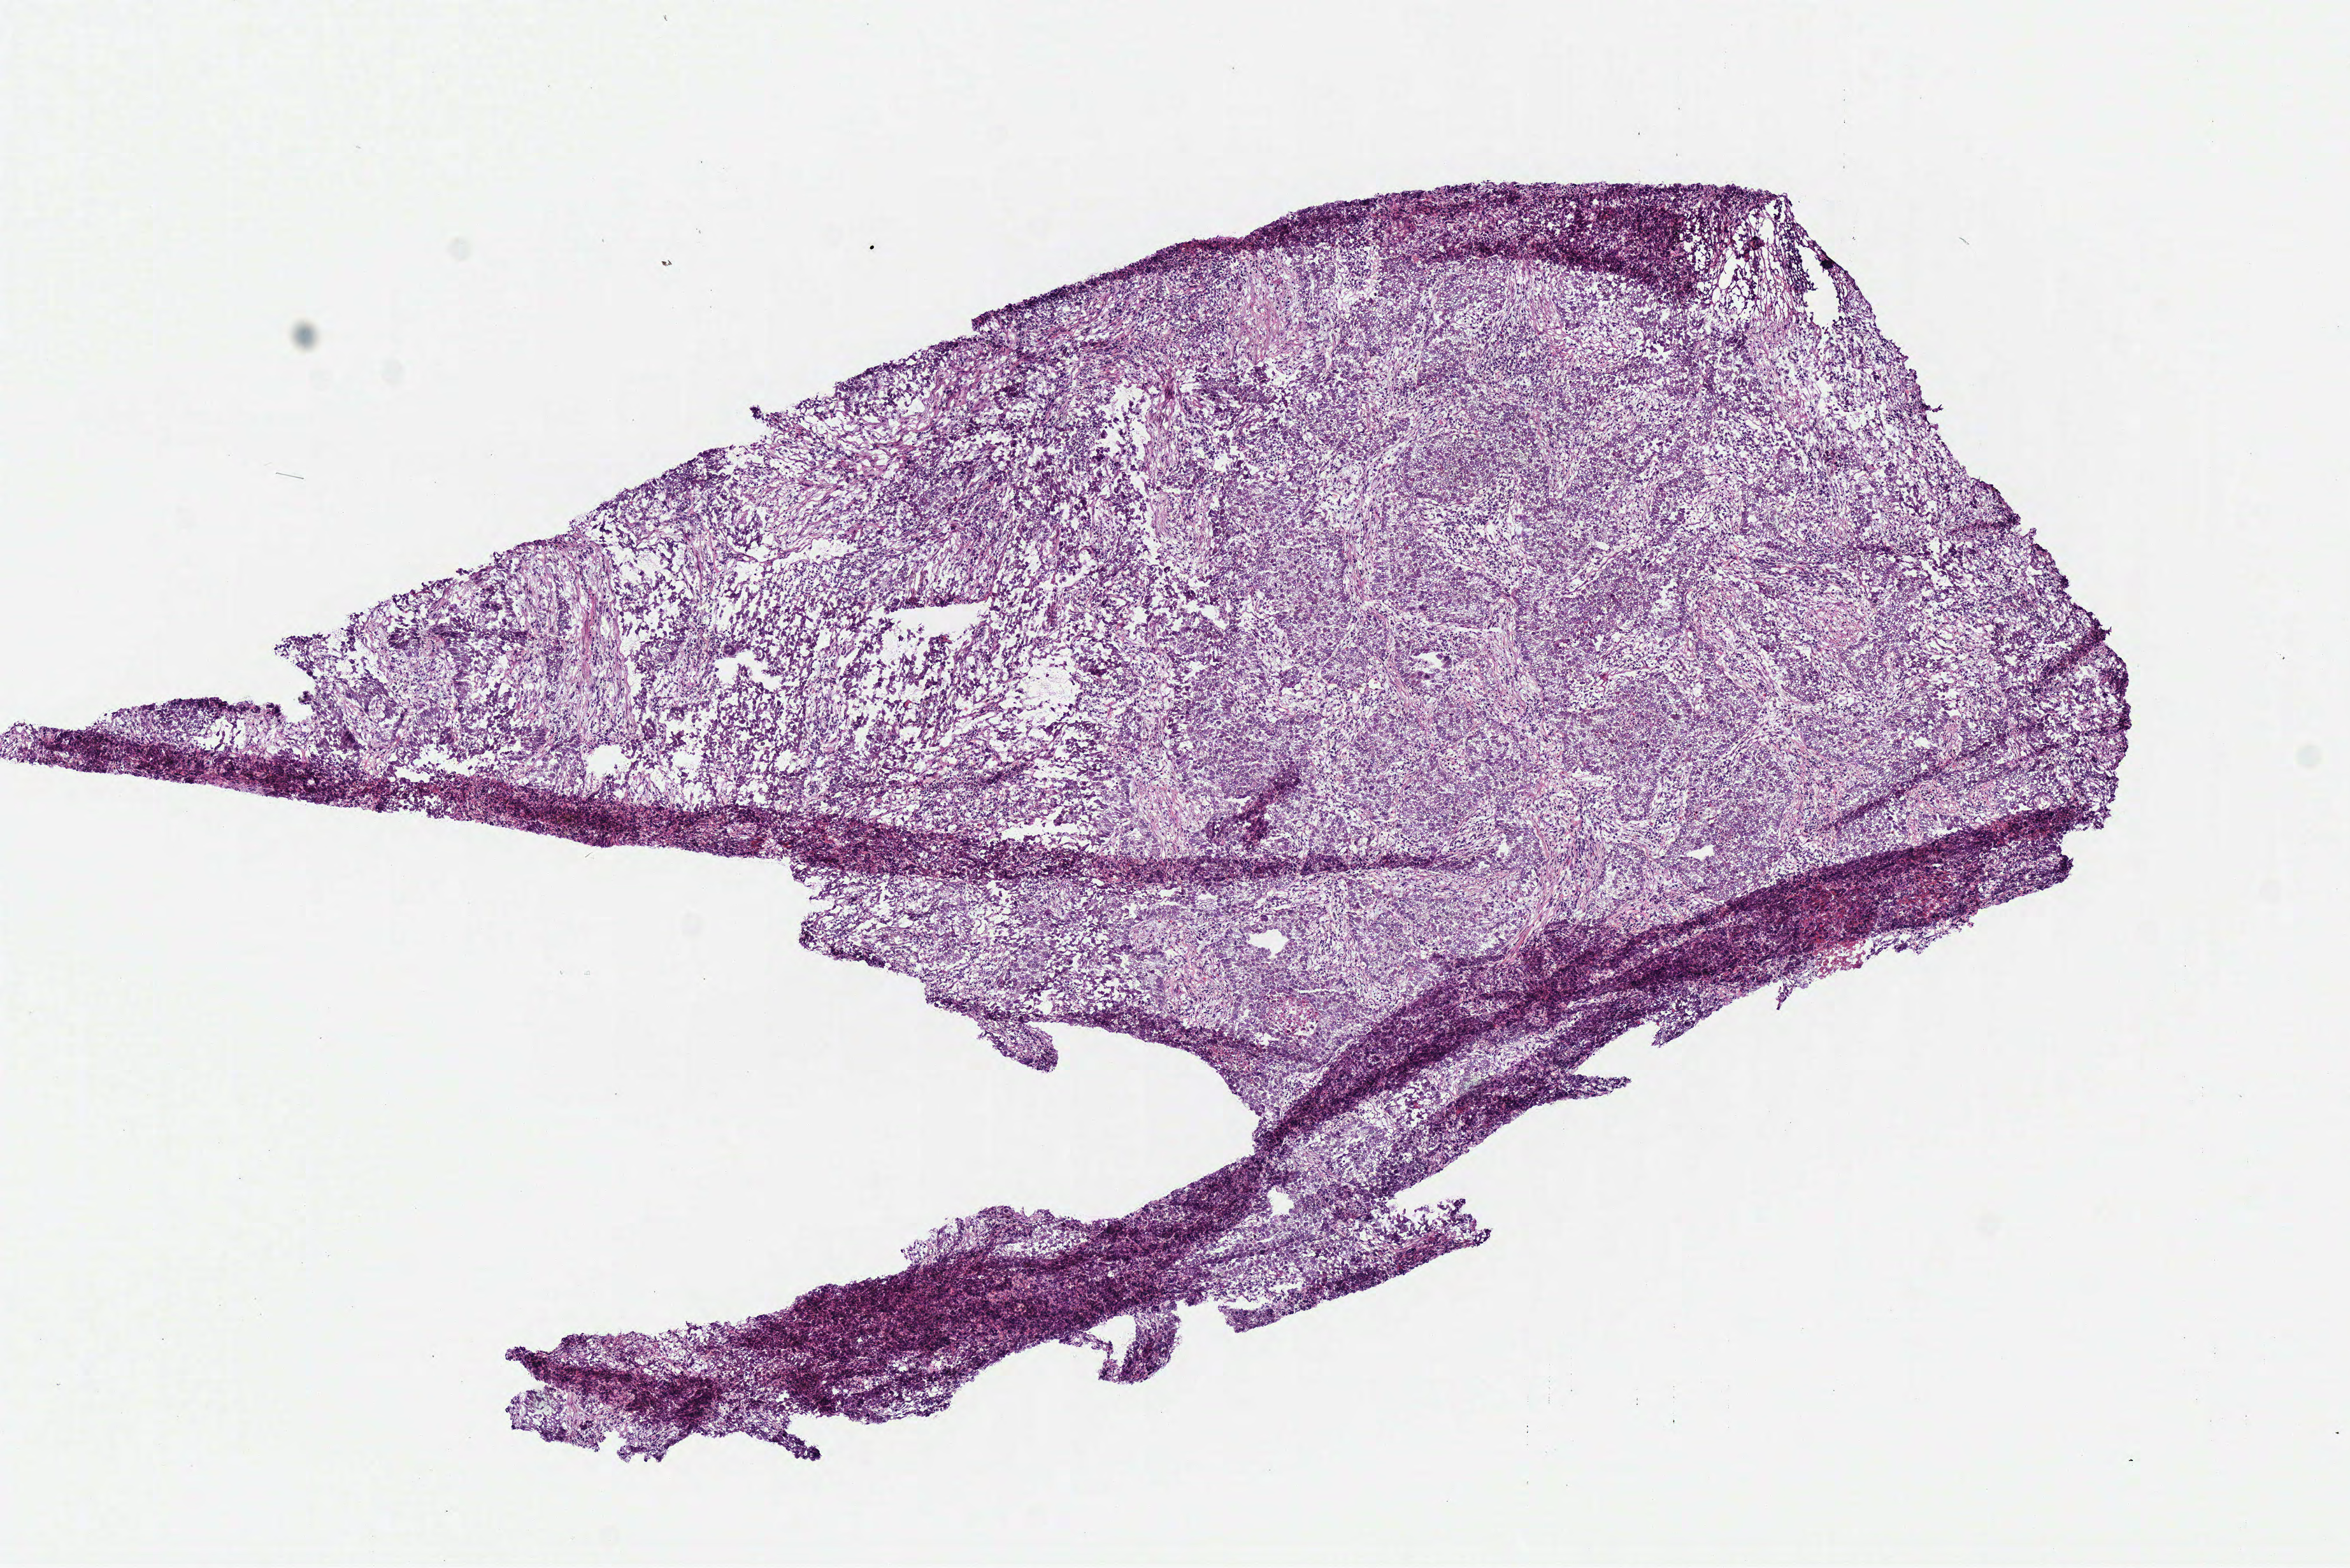
H&E whole-slide image, shown as a low-resolution overview of the whole scanned area (about 7.3 x 4.8 mm, from a 40x scan); frozen section; sample: primary tumour, lung. Patient sex: female. Pathologist review of this section (percent, as recorded): tumour cells 100%, tumour nuclei 80%, normal cells 0%, stromal cells 0%, necrosis 0%. Inflammatory infiltration, as recorded: lymphocyte infiltration 7%, monocyte infiltration 2%, neutrophil infiltration 7%.
- histologic diagnosis: Adenocarcinoma, NOS
- AJCC pathologic stage: IB